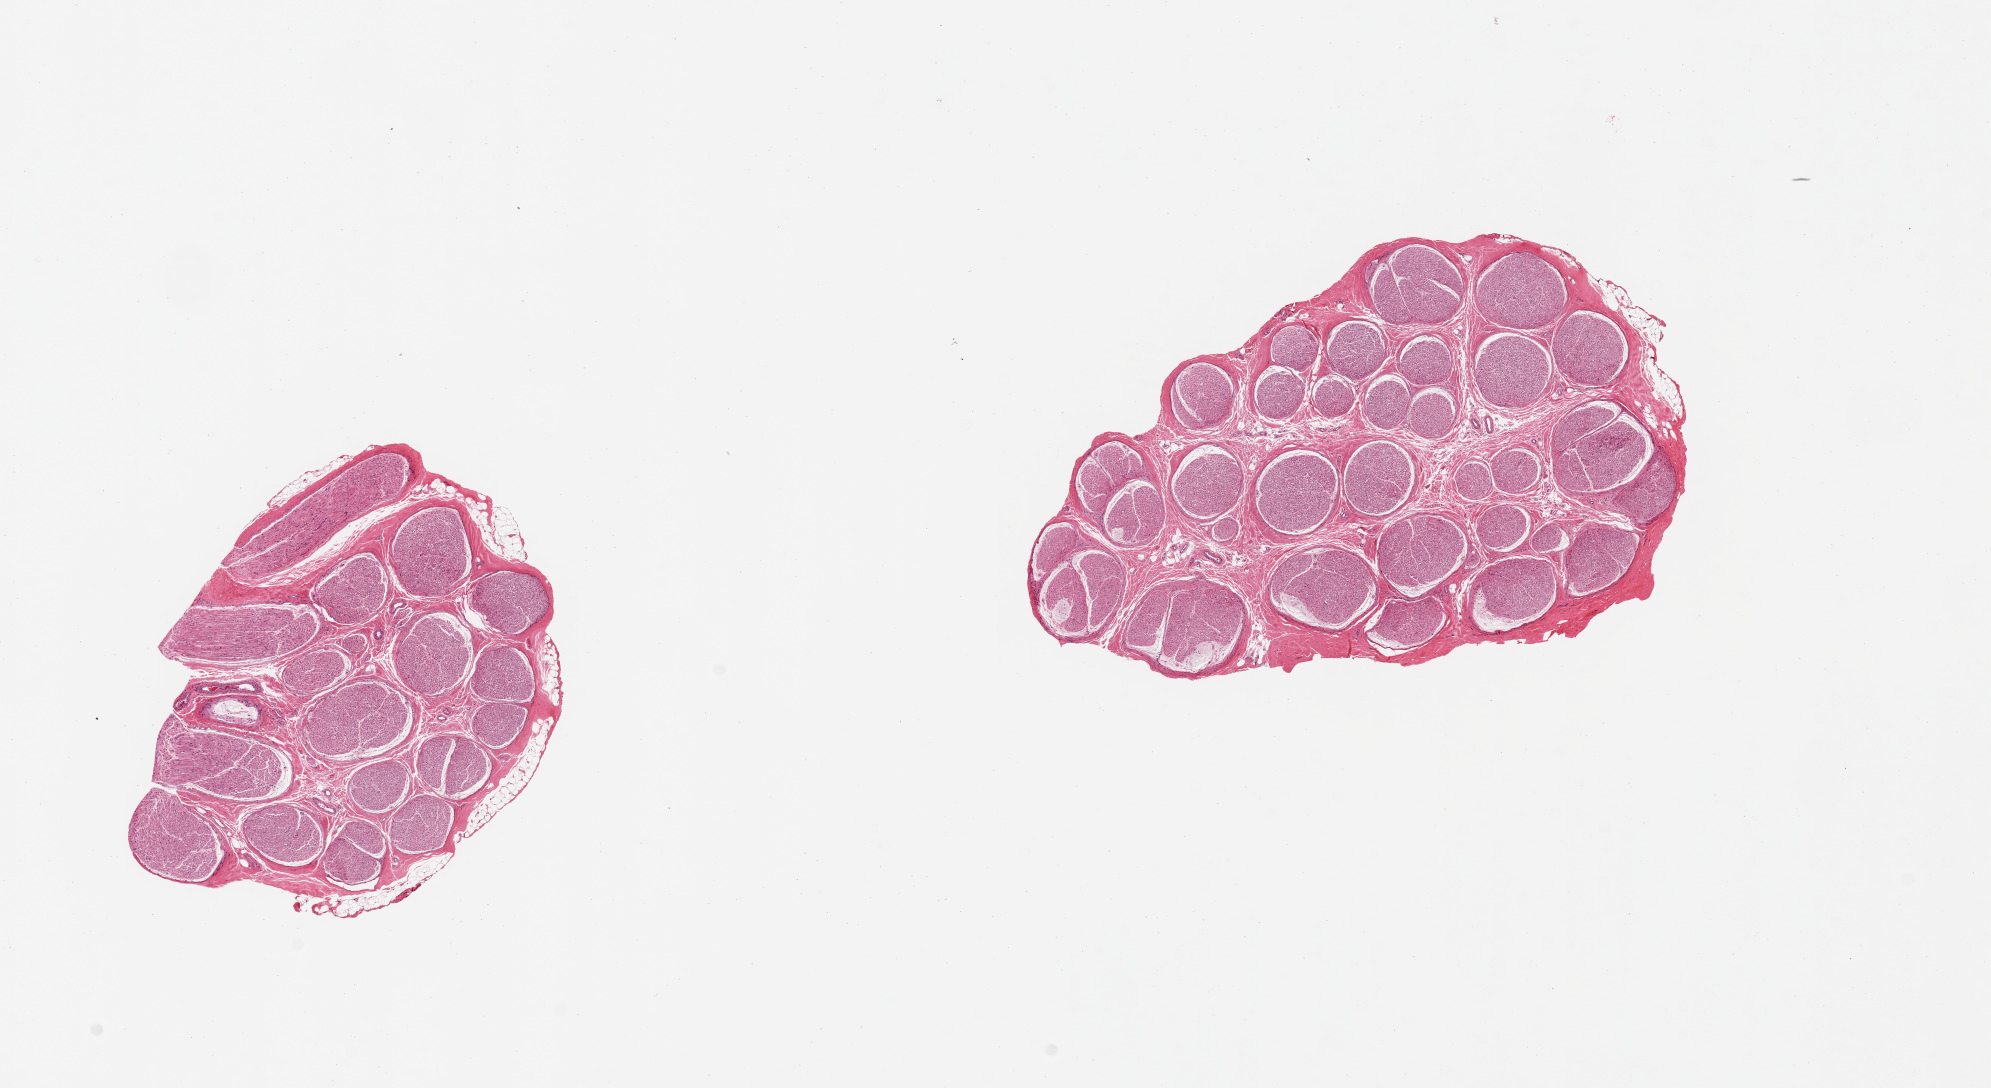
Whole-slide image, haematoxylin and eosin stain, a low-resolution overview of the entire scanned area, about 15.8 x 8.6 mm; PAXgene-fixed paraffin-embedded (PFPE) section; target tissue: tibial nerve; donor tissue sample. Donor sex: female.
• review note (as recorded): 2 pieces; well trimmed